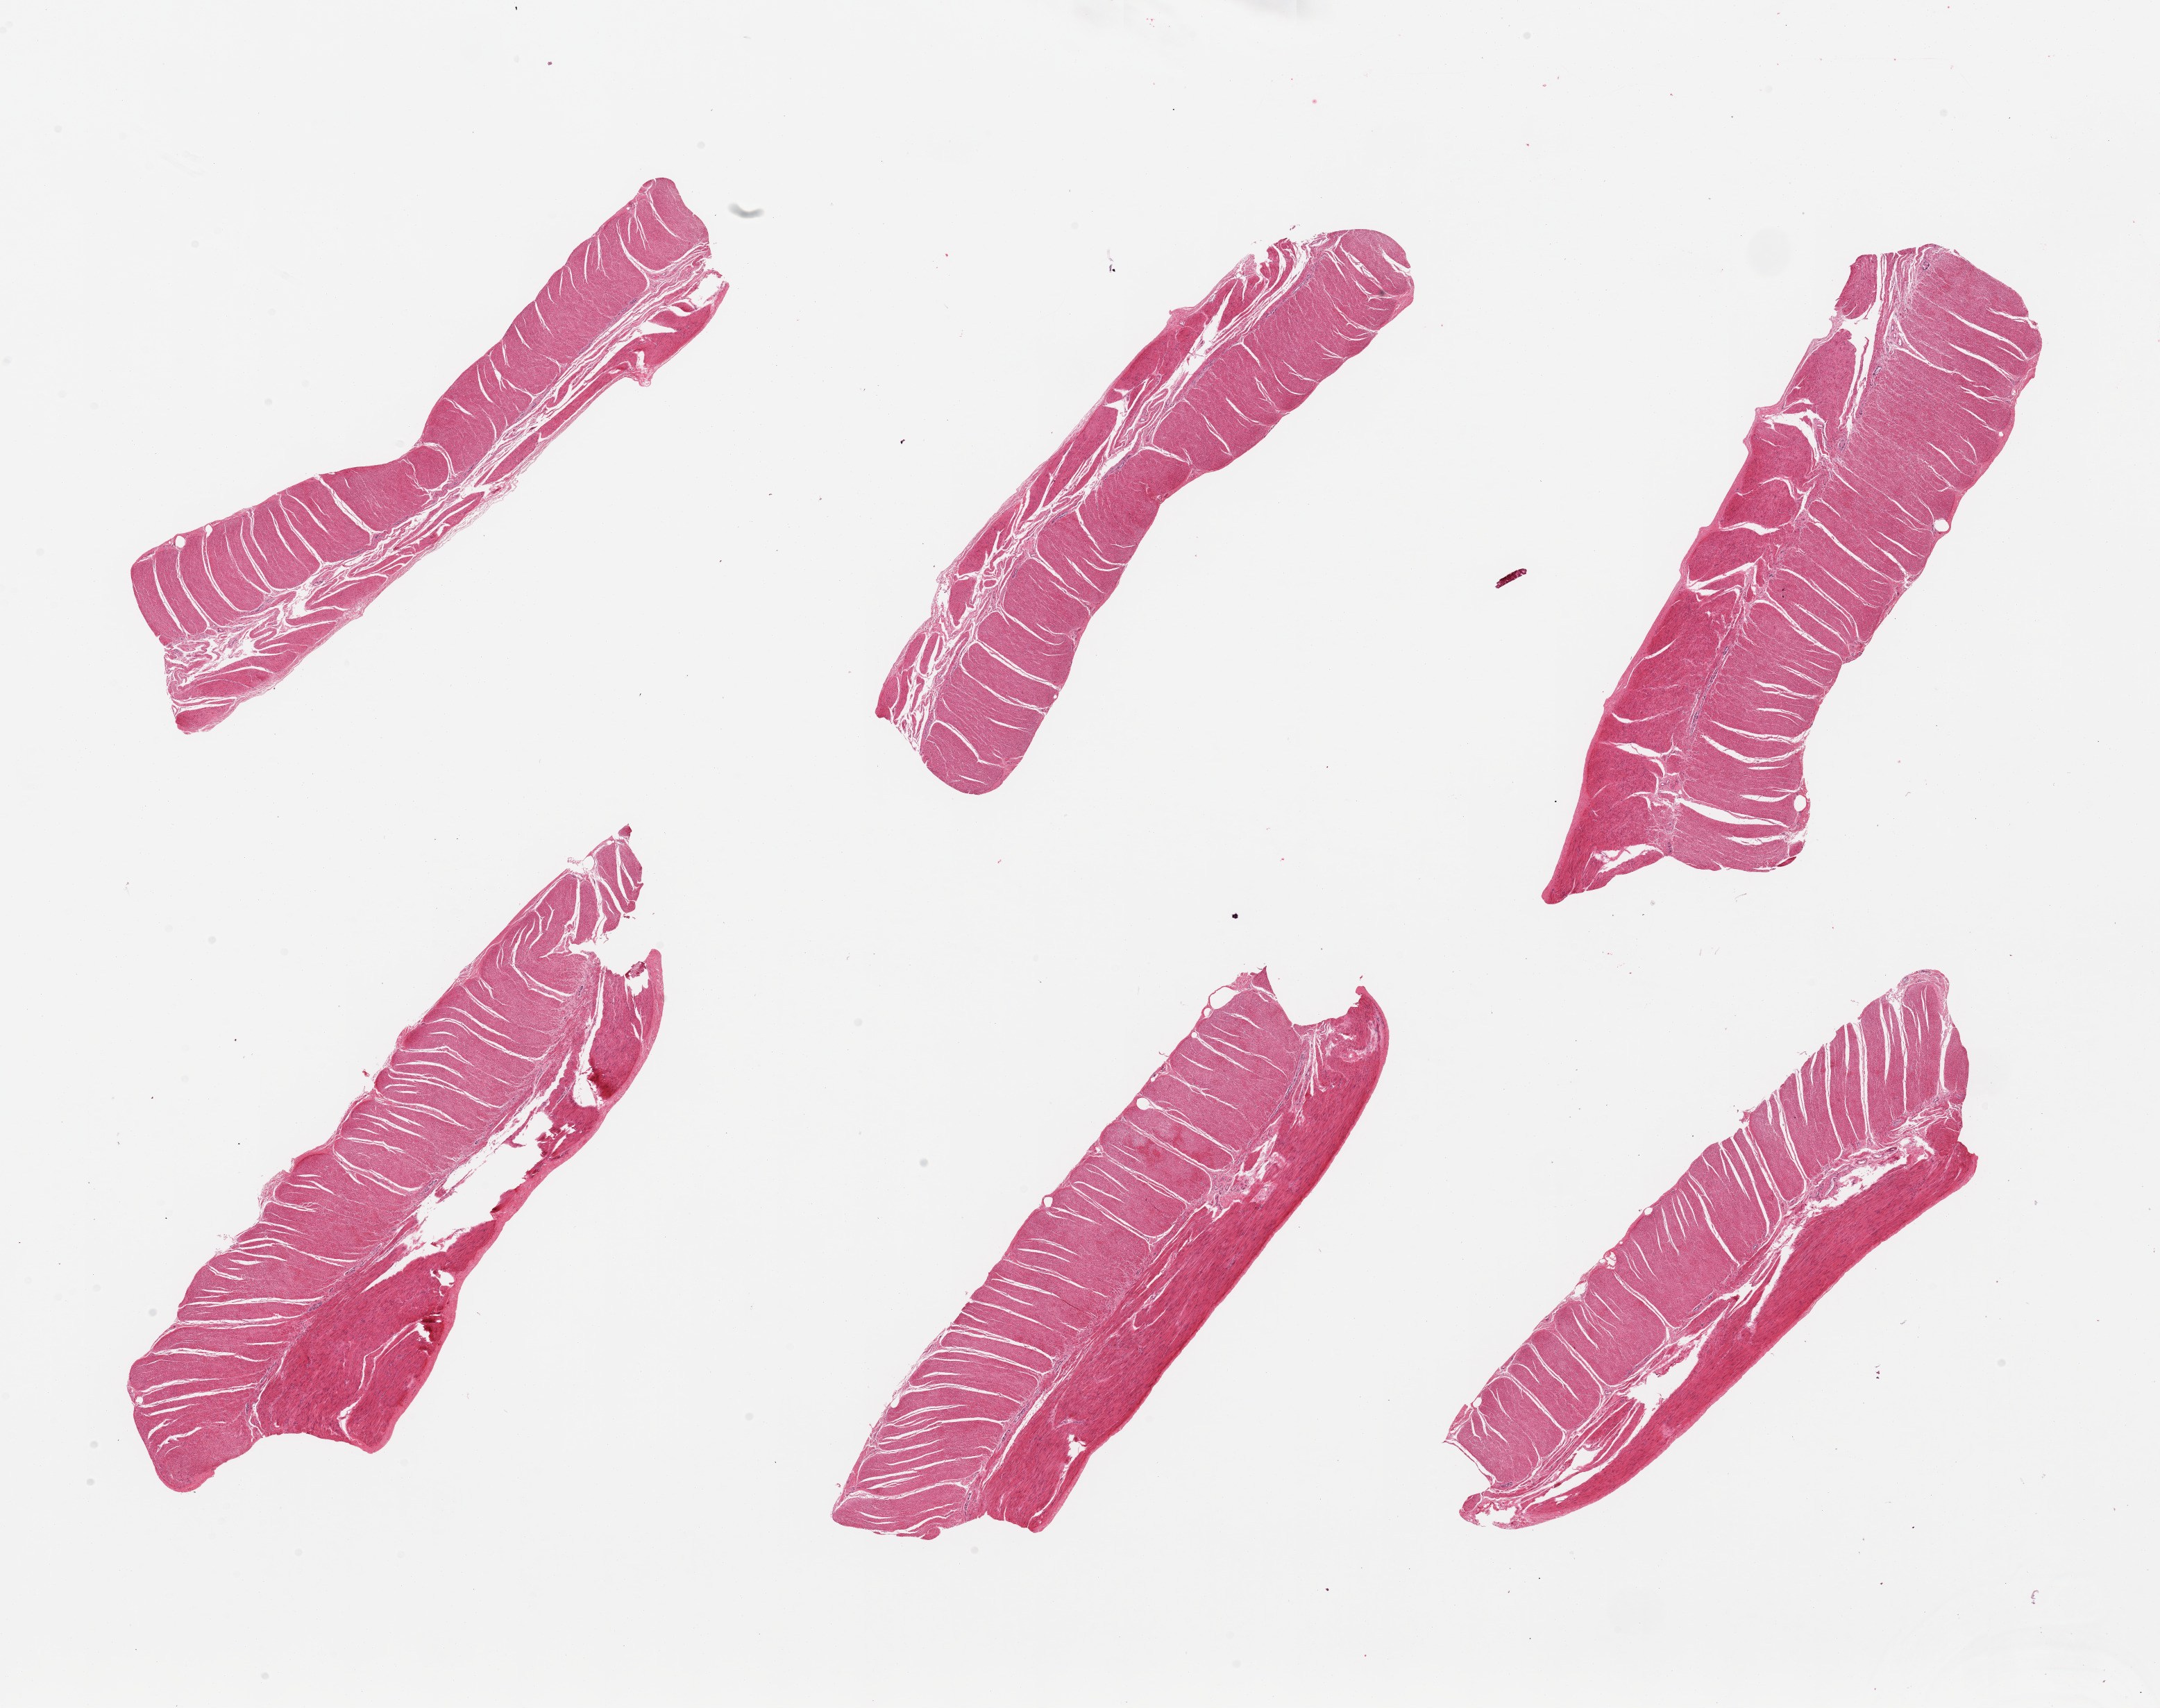
Digitized haematoxylin and eosin-stained section, a low-resolution overview of the entire scanned area, about 24.6 x 19.5 mm (acquisition: 20x scan), PAXgene-fixed, paraffin-embedded tissue, section of sigmoid colon (target tissue), donor tissue sample.
- pathologist's review note for this sample: 6 pieces, all target muscularis